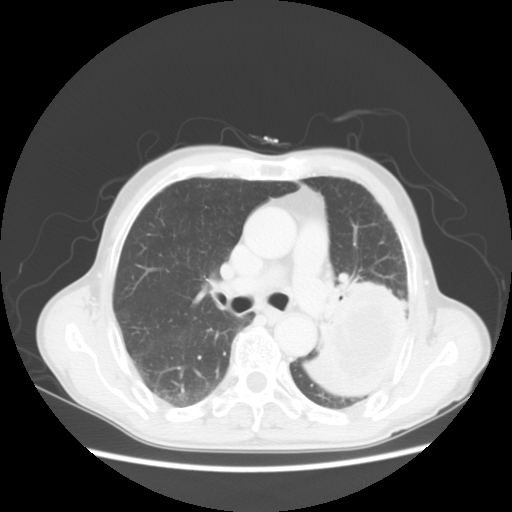
Chest CT, one axial slice; reconstruction kernel STANDARD; 120 kVp; lung window (W 1500 / L -600 HU); 5 mm slice thickness; 512 × 512 image matrix, field of view 360 × 360 mm. Patient: male, 64 years. From the clinical record (not read from this slice): clinical TNM (as recorded): T4 N0 M0.
Outlined on this slice (rectangle marked by the reading radiologist):
- lung tumour (recorded histology: squamous cell carcinoma): bounding box (x1, y1, x2, y2) in pixels: (287, 262, 419, 420)